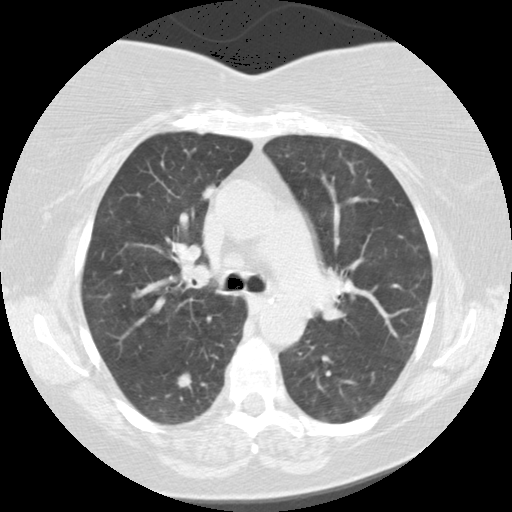
Chest CT (low-dose screening protocol), one axial image, second screening round (one year after baseline), lung window (W 1500 / L -600 HU), 2.5 mm slice thickness, standard (soft-tissue) reconstruction kernel (STANDARD). Female participant, aged 62 years at enrolment. Current smoker at enrolment.
Expert reader's lesion annotation, bounding box (x1, y1, x2, y2) in pixels: (178, 171, 232, 215). The screening reader recorded 3 non-calcified nodules or masses ≥4 mm on this exam; which of them this box marks is not recorded. Later outcome: lung cancer diagnosed 376 days after this screen (after the third annual screen) — adenocarcinoma, NOS, right upper lobe, poorly differentiated (G3), stage IB (AJCC 6th edition), 12 mm at pathology.